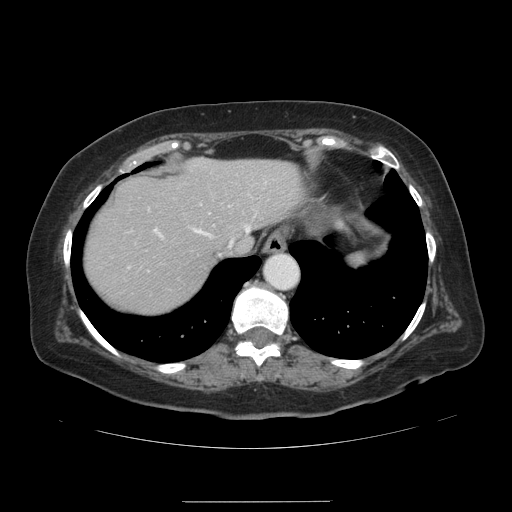
Contrast-enhanced abdominal CT, one axial slice; 120 kVp; intravenous contrast given; soft-tissue window (W 400 / L 40 HU); 2.5 mm slice thickness; 512 × 512 image matrix, field of view 393 × 393 mm. Female patient, age 74 years. From the clinical record (not read from this slice): diagnosis: colorectal cancer liver metastases, imaged before liver resection; multiple liver metastases: yes; largest metastasis: 7 cm.
Annotated regions visible in this slice (manually delineated by an expert):
- hepatic veins: box from (x=195, y=228) to (x=248, y=255) px
- liver: (x=85, y=159)–(x=301, y=312)
- planned liver remnant (the part of the liver to remain after resection): (x=85, y=159)–(x=301, y=312)
- portal vein (with intrahepatic branches): (x=128, y=228)–(x=161, y=267)